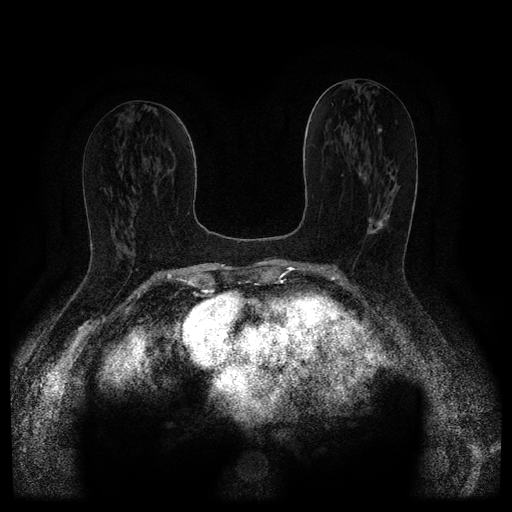
Breast MRI (dynamic contrast-enhanced, multi-phase), one axial slice; position 51 of 116 along the scan axis; dynamic contrast-enhanced series, time point 2 of 5 at this slice position (early post-contrast); 1.5 T; TE 2.6 ms, TR 5.4 ms; 2 mm slice thickness; 512 × 512 image matrix, field of view 340 × 340 mm. Patient: female, 67 years.
Annotated regions visible in this slice (semi-automatically segmented with operator editing):
- breast lesion (labelled 'tumour' in the annotation; benign lesions carry a separate 'benign' label): bounding box (x1, y1, x2, y2) in pixels: (367, 213, 389, 234)